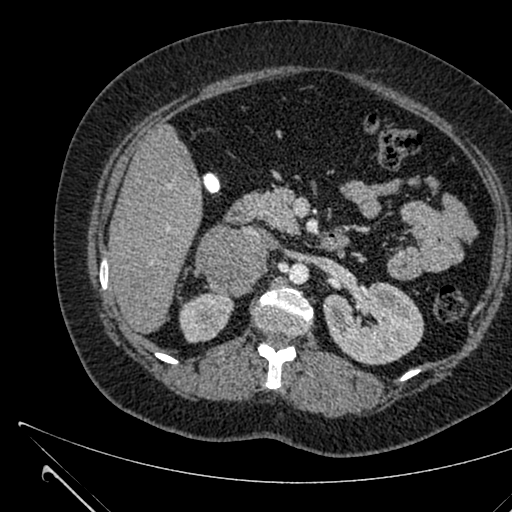
Contrast-enhanced abdominal CT, one axial slice; position 373 of 731 along the scan axis; intravenous contrast given; soft-tissue window (W 400 / L 40 HU); 1 mm slice thickness; 512 × 512 image matrix, field of view 376 × 376 mm. Patient: female, 36 years. From the clinical record (not read from this slice): diagnosis: adrenocortical carcinoma; tumour side: right adrenal; tumour size at pathology: 10 cm; Ki-67 index: 20 %; stage (as recorded): 4.
Annotated regions visible in this slice (semi-automatically segmented with operator editing):
- mass: bounding box <194,224,264,296> (left, top, right, bottom; pixels)